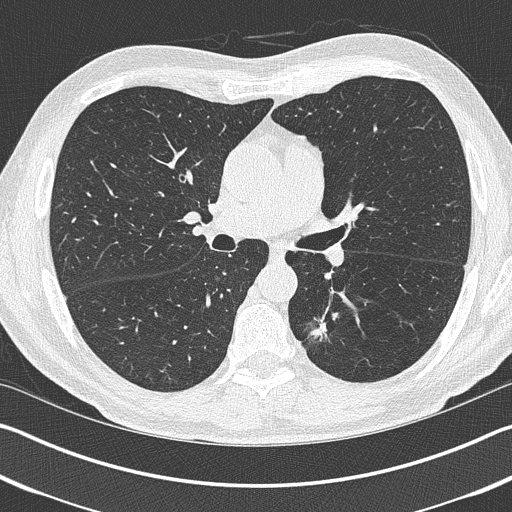
Axial slice from a low-dose chest CT screening exam, baseline annual screen, lung window (W 1500 / L -600 HU). Male participant, aged 69 years at enrolment.
- Expert-annotated lung lesion, box from (x=300, y=308) to (x=355, y=361) px.
- Reader record for this screening exam (exam-level; its link to the box is not recorded): non-calcified nodule or mass ≥4 mm, left upper lobe, 19 × 19 mm, spiculated (stellate) margins, pre-existing on the prior screen: yes.
- Official screen result: positive, change unspecified: nodule(s) >= 4 mm or enlarging nodule(s), mass(es), or other non-specific abnormalities suspicious for lung cancer.
- Lung cancer was diagnosed 202 days after this screen: non-small cell carcinoma, left lower lobe, stage IIIA (AJCC 6th edition), 20 mm at pathology.